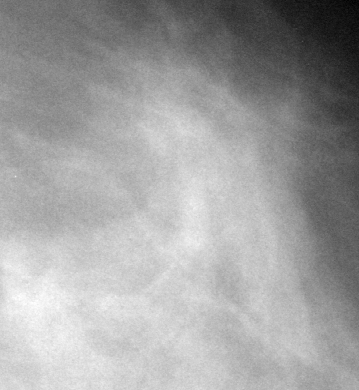
Region of interest cut from a scanned film mammogram (one marked finding), left breast, CC view, BI-RADS breast density category 1 (scale 1–4).
Marked abnormality: mass, shape irregular, margins spiculated; BI-RADS assessment category 4; benign; no additional work-up was recommended (benign without callback).